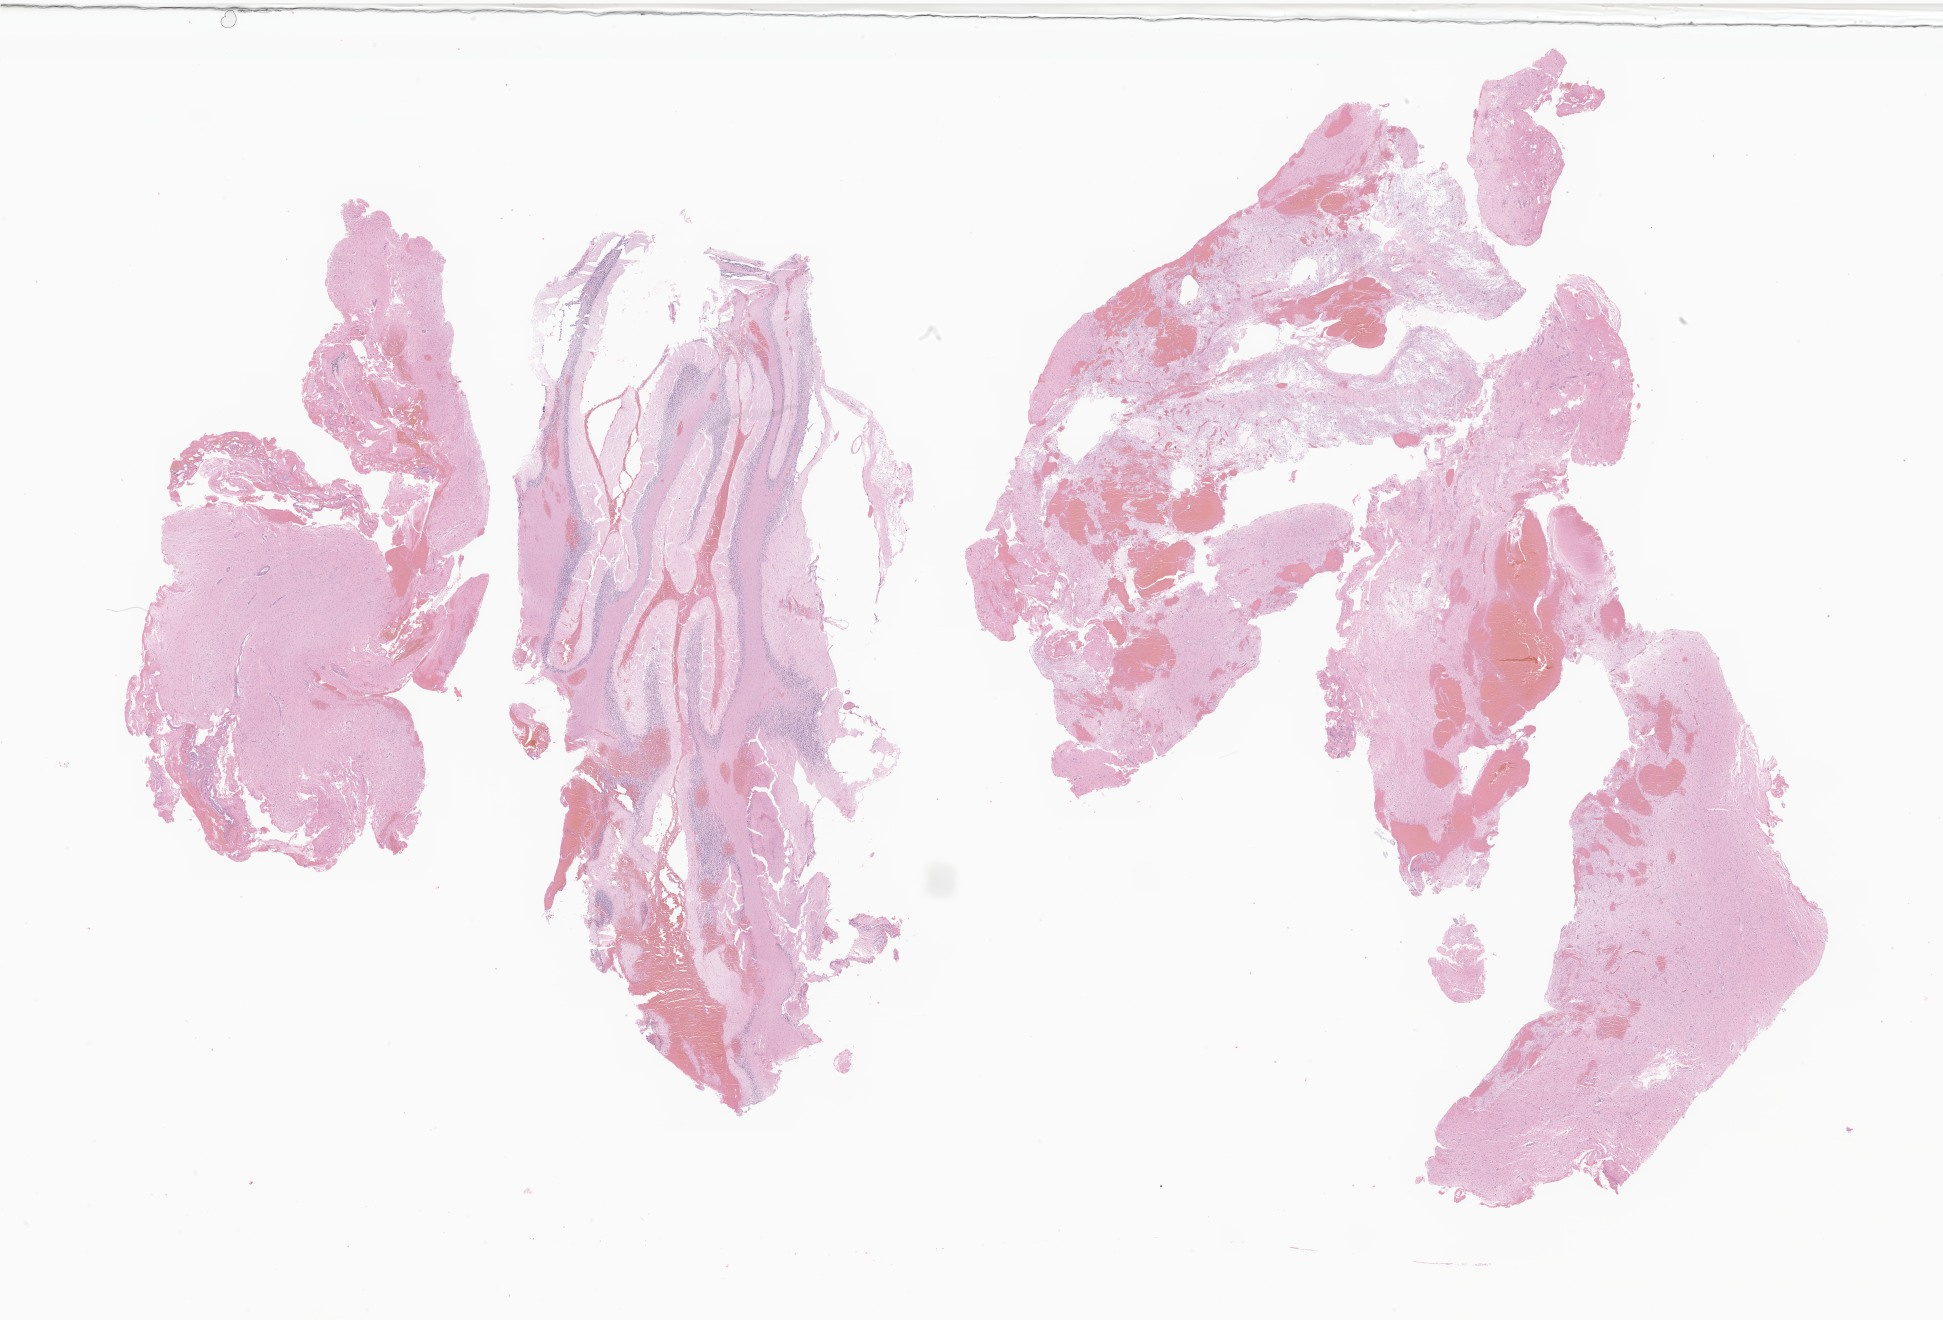
Whole-slide image, haematoxylin and eosin stain of tumor tissue from the brain — whole scanned area (about 32.8 x 22.3 mm) shown as a low-resolution overview. Formalin-fixed, paraffin-embedded (FFPE) tissue. Female patient, age 147 months.
* diagnosis: Pilocytic astrocytoma